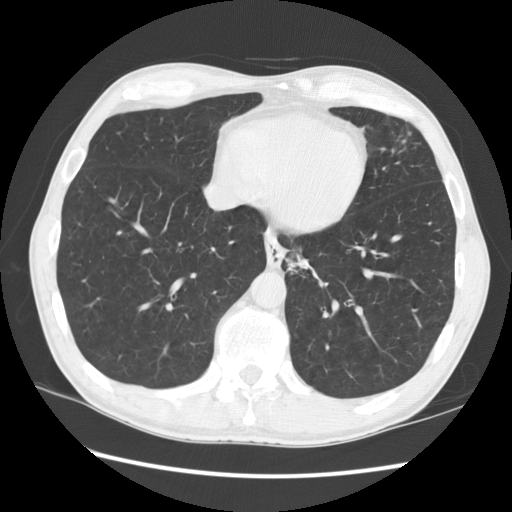
Axial slice from a low-dose chest CT screening exam; baseline annual screen; lung window (W 1500 / L -600 HU); 2.5 mm slice thickness; 120 kVp. Male, age 57 years at enrolment. Current smoker at enrolment.
• Expert reader's lesion annotation, bounding box <270,240,336,301> (left, top, right, bottom; pixels).
• The screening reader recorded 2 non-calcified nodules or masses ≥4 mm on this exam (left lower lobe, lingula); which of them this box marks is not recorded.
• Official screen result: positive, change unspecified: nodule(s) >= 4 mm or enlarging nodule(s), mass(es), or other non-specific abnormalities suspicious for lung cancer.
• Lung cancer was diagnosed 95 days after this screen: squamous cell carcinoma, NOS, left lower lobe, moderately differentiated (G2), stage IB (AJCC 6th edition), 35 mm at pathology.